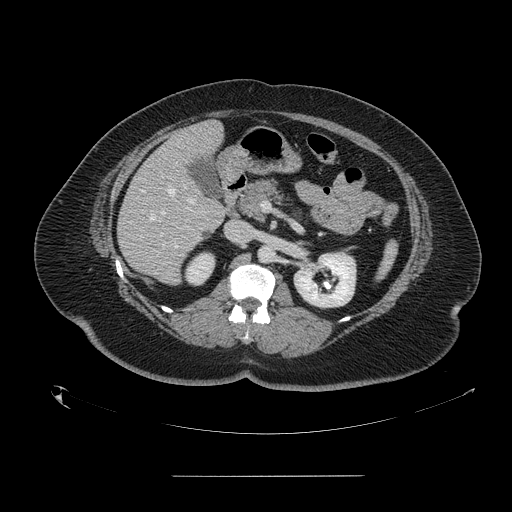
Contrast-enhanced abdominal CT, one axial slice; slice 75 of 164 in the series (ordered by position); intravenous contrast given; soft-tissue window (W 400 / L 40 HU); 2.5 mm slice thickness; 512 × 512 image matrix, field of view 495 × 495 mm. Female patient, age 52 years. From the clinical record (not read from this slice): diagnosis: colorectal cancer liver metastases, imaged before liver resection; multiple liver metastases: yes; largest metastasis: 3.5 cm; disease in both lobes: no.
Structures marked on this image (expert manual segmentation):
- hepatic veins: box from (x=140, y=189) to (x=192, y=230) px
- liver: (x=118, y=122)–(x=226, y=284)
- planned liver remnant (the part of the liver to remain after resection): (x=177, y=122)–(x=223, y=162)
- portal vein (with intrahepatic branches): (x=161, y=175)–(x=194, y=235)
- liver metastasis: (x=203, y=231)–(x=210, y=238)